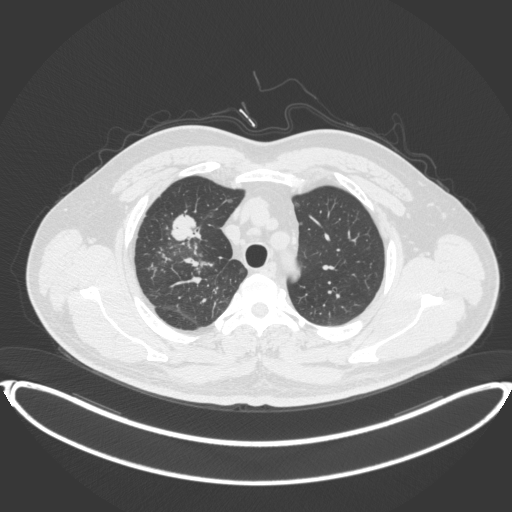
Chest CT, one axial slice. Slice 305 of 399 in the series (ordered by position). 120 kVp. Lung window (W 1500 / L -600 HU). 1 mm slice thickness. 512 × 512 image matrix, field of view 445 × 445 mm. Male patient, age 53 years. Case-level facts recorded for this patient, not image findings: clinical TNM (as recorded): T2a N0 M0.
Structures marked on this image (bounding box drawn by a radiologist):
- lung tumour (recorded histology: adenocarcinoma): bounding box [x1, y1, x2, y2] px = [168, 213, 206, 244]